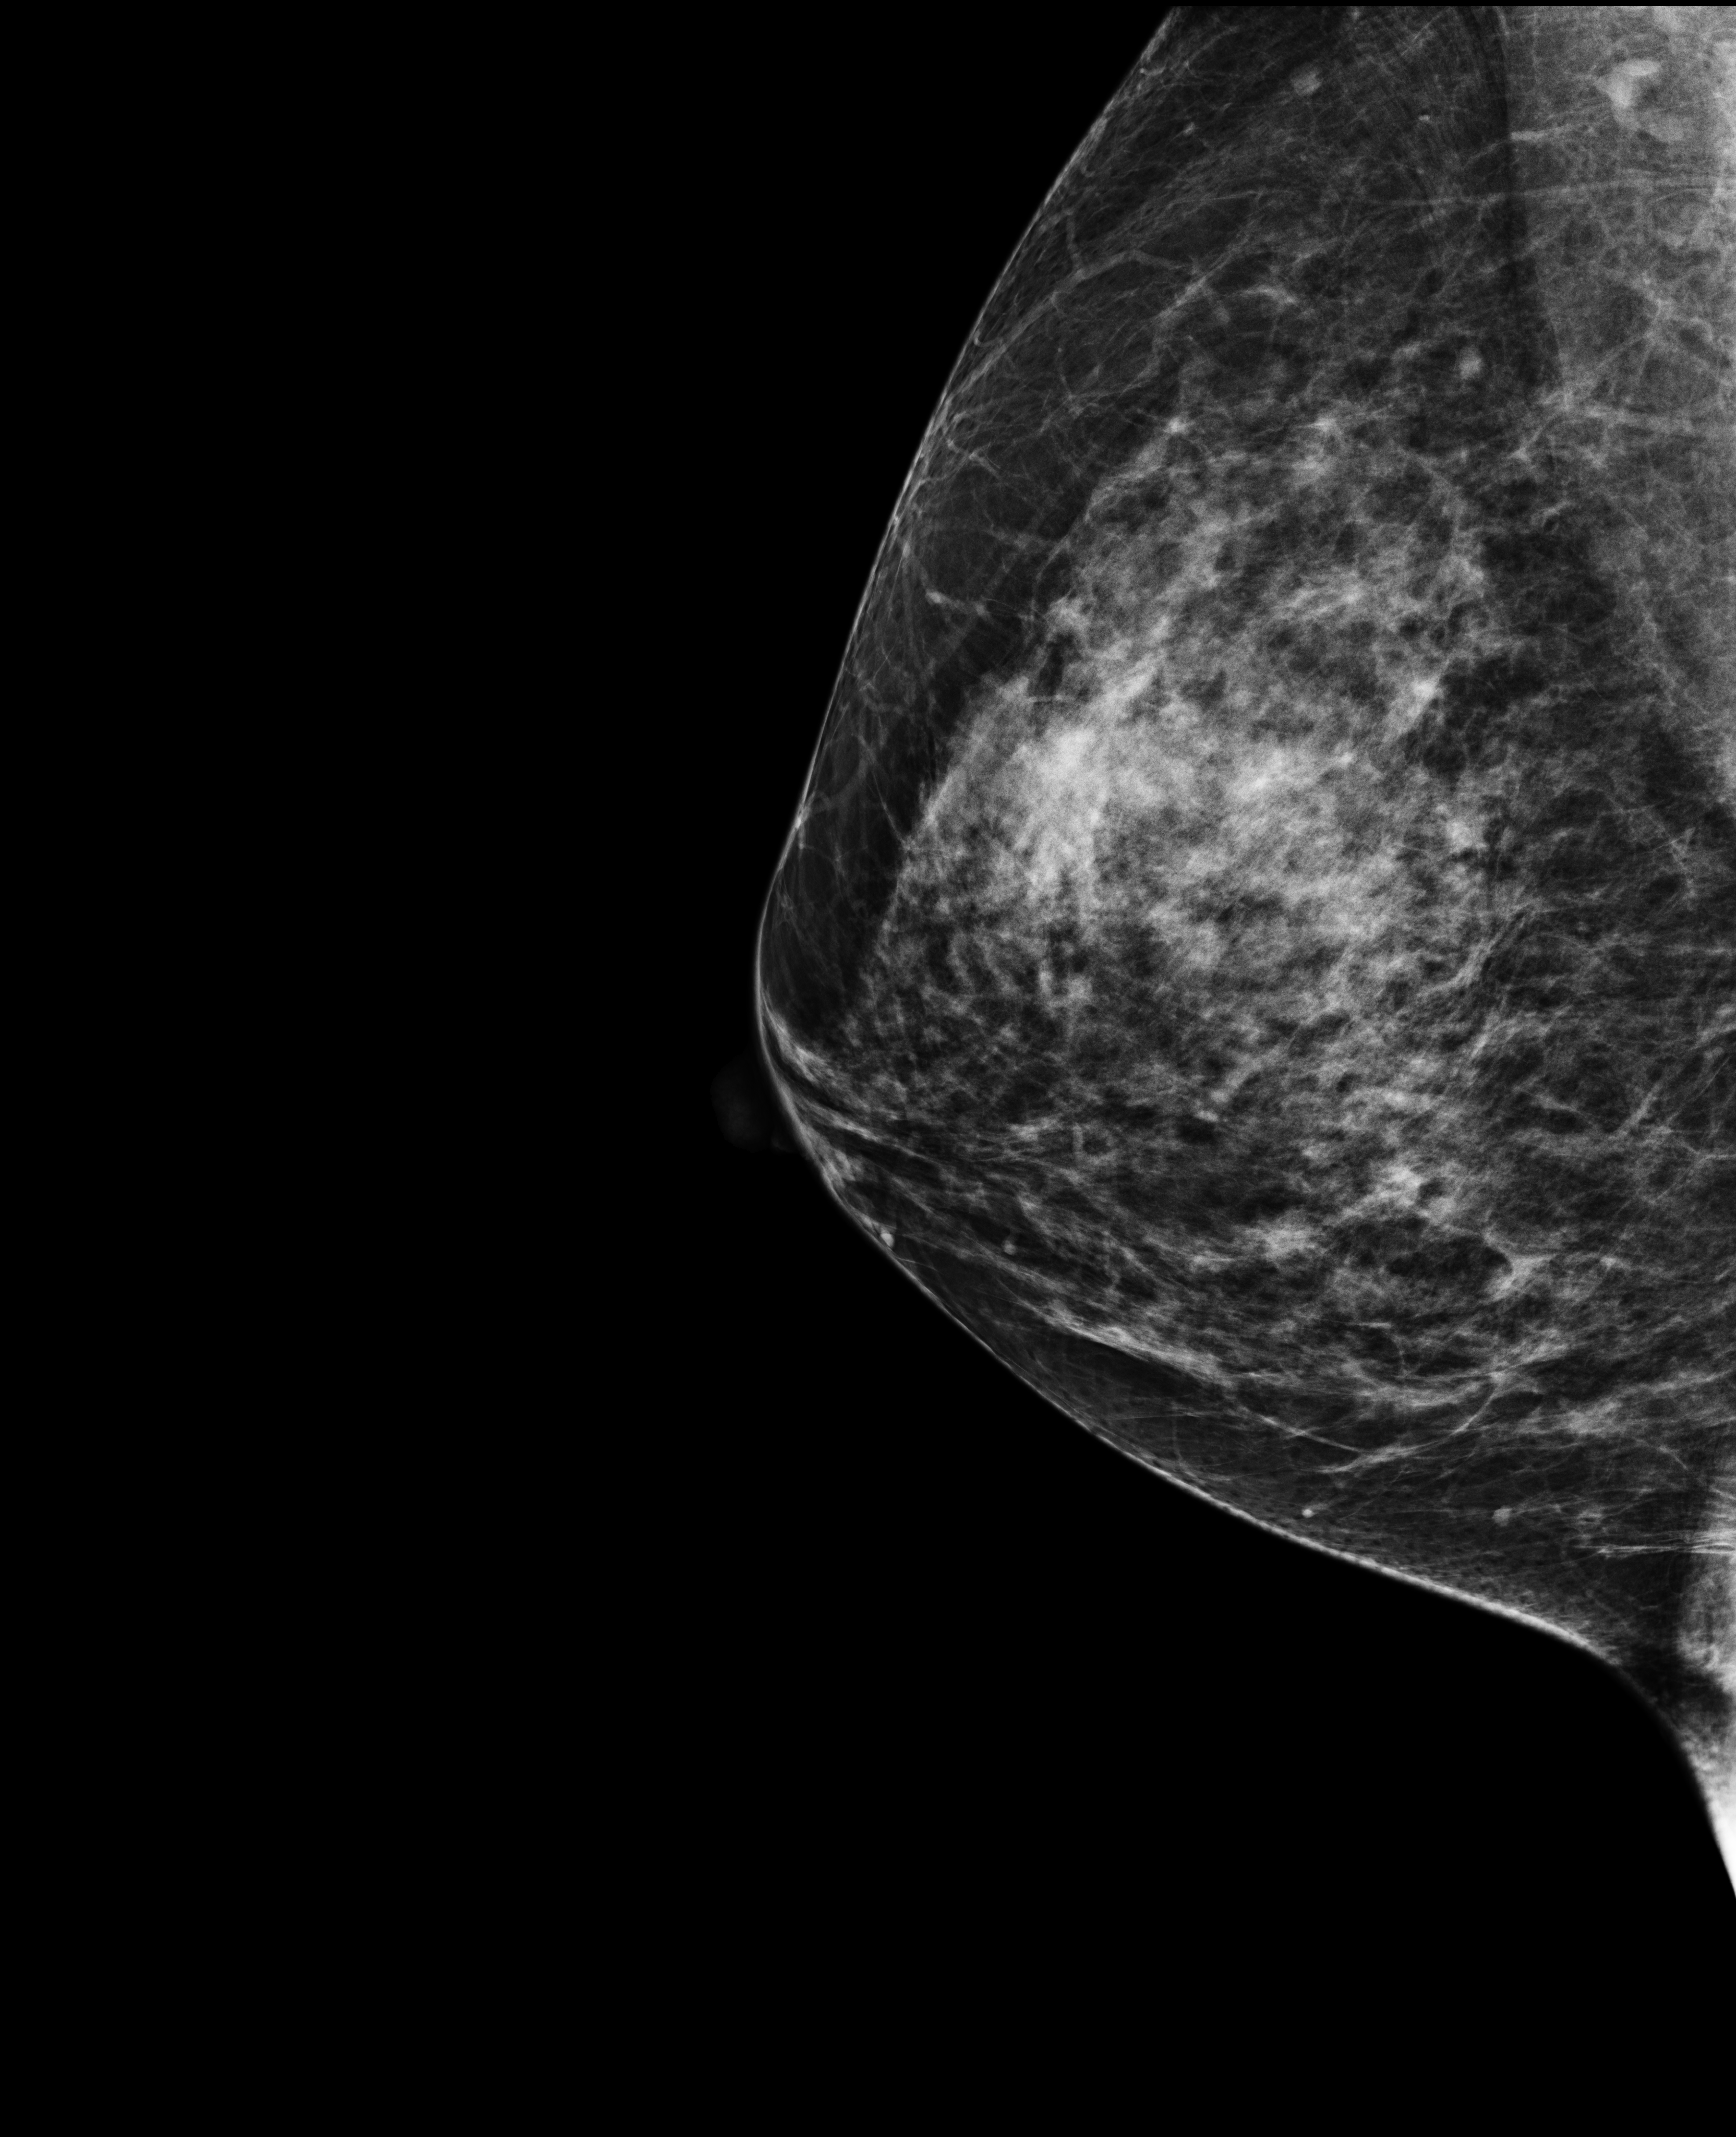
Screening examination, compressed breast thickness 74 mm, system: Selenia Dimensions. Patient aged 47 years (female).
Image type: full-field digital mammogram. Breast: right. Projection: MLO view, infra-mammary fold.